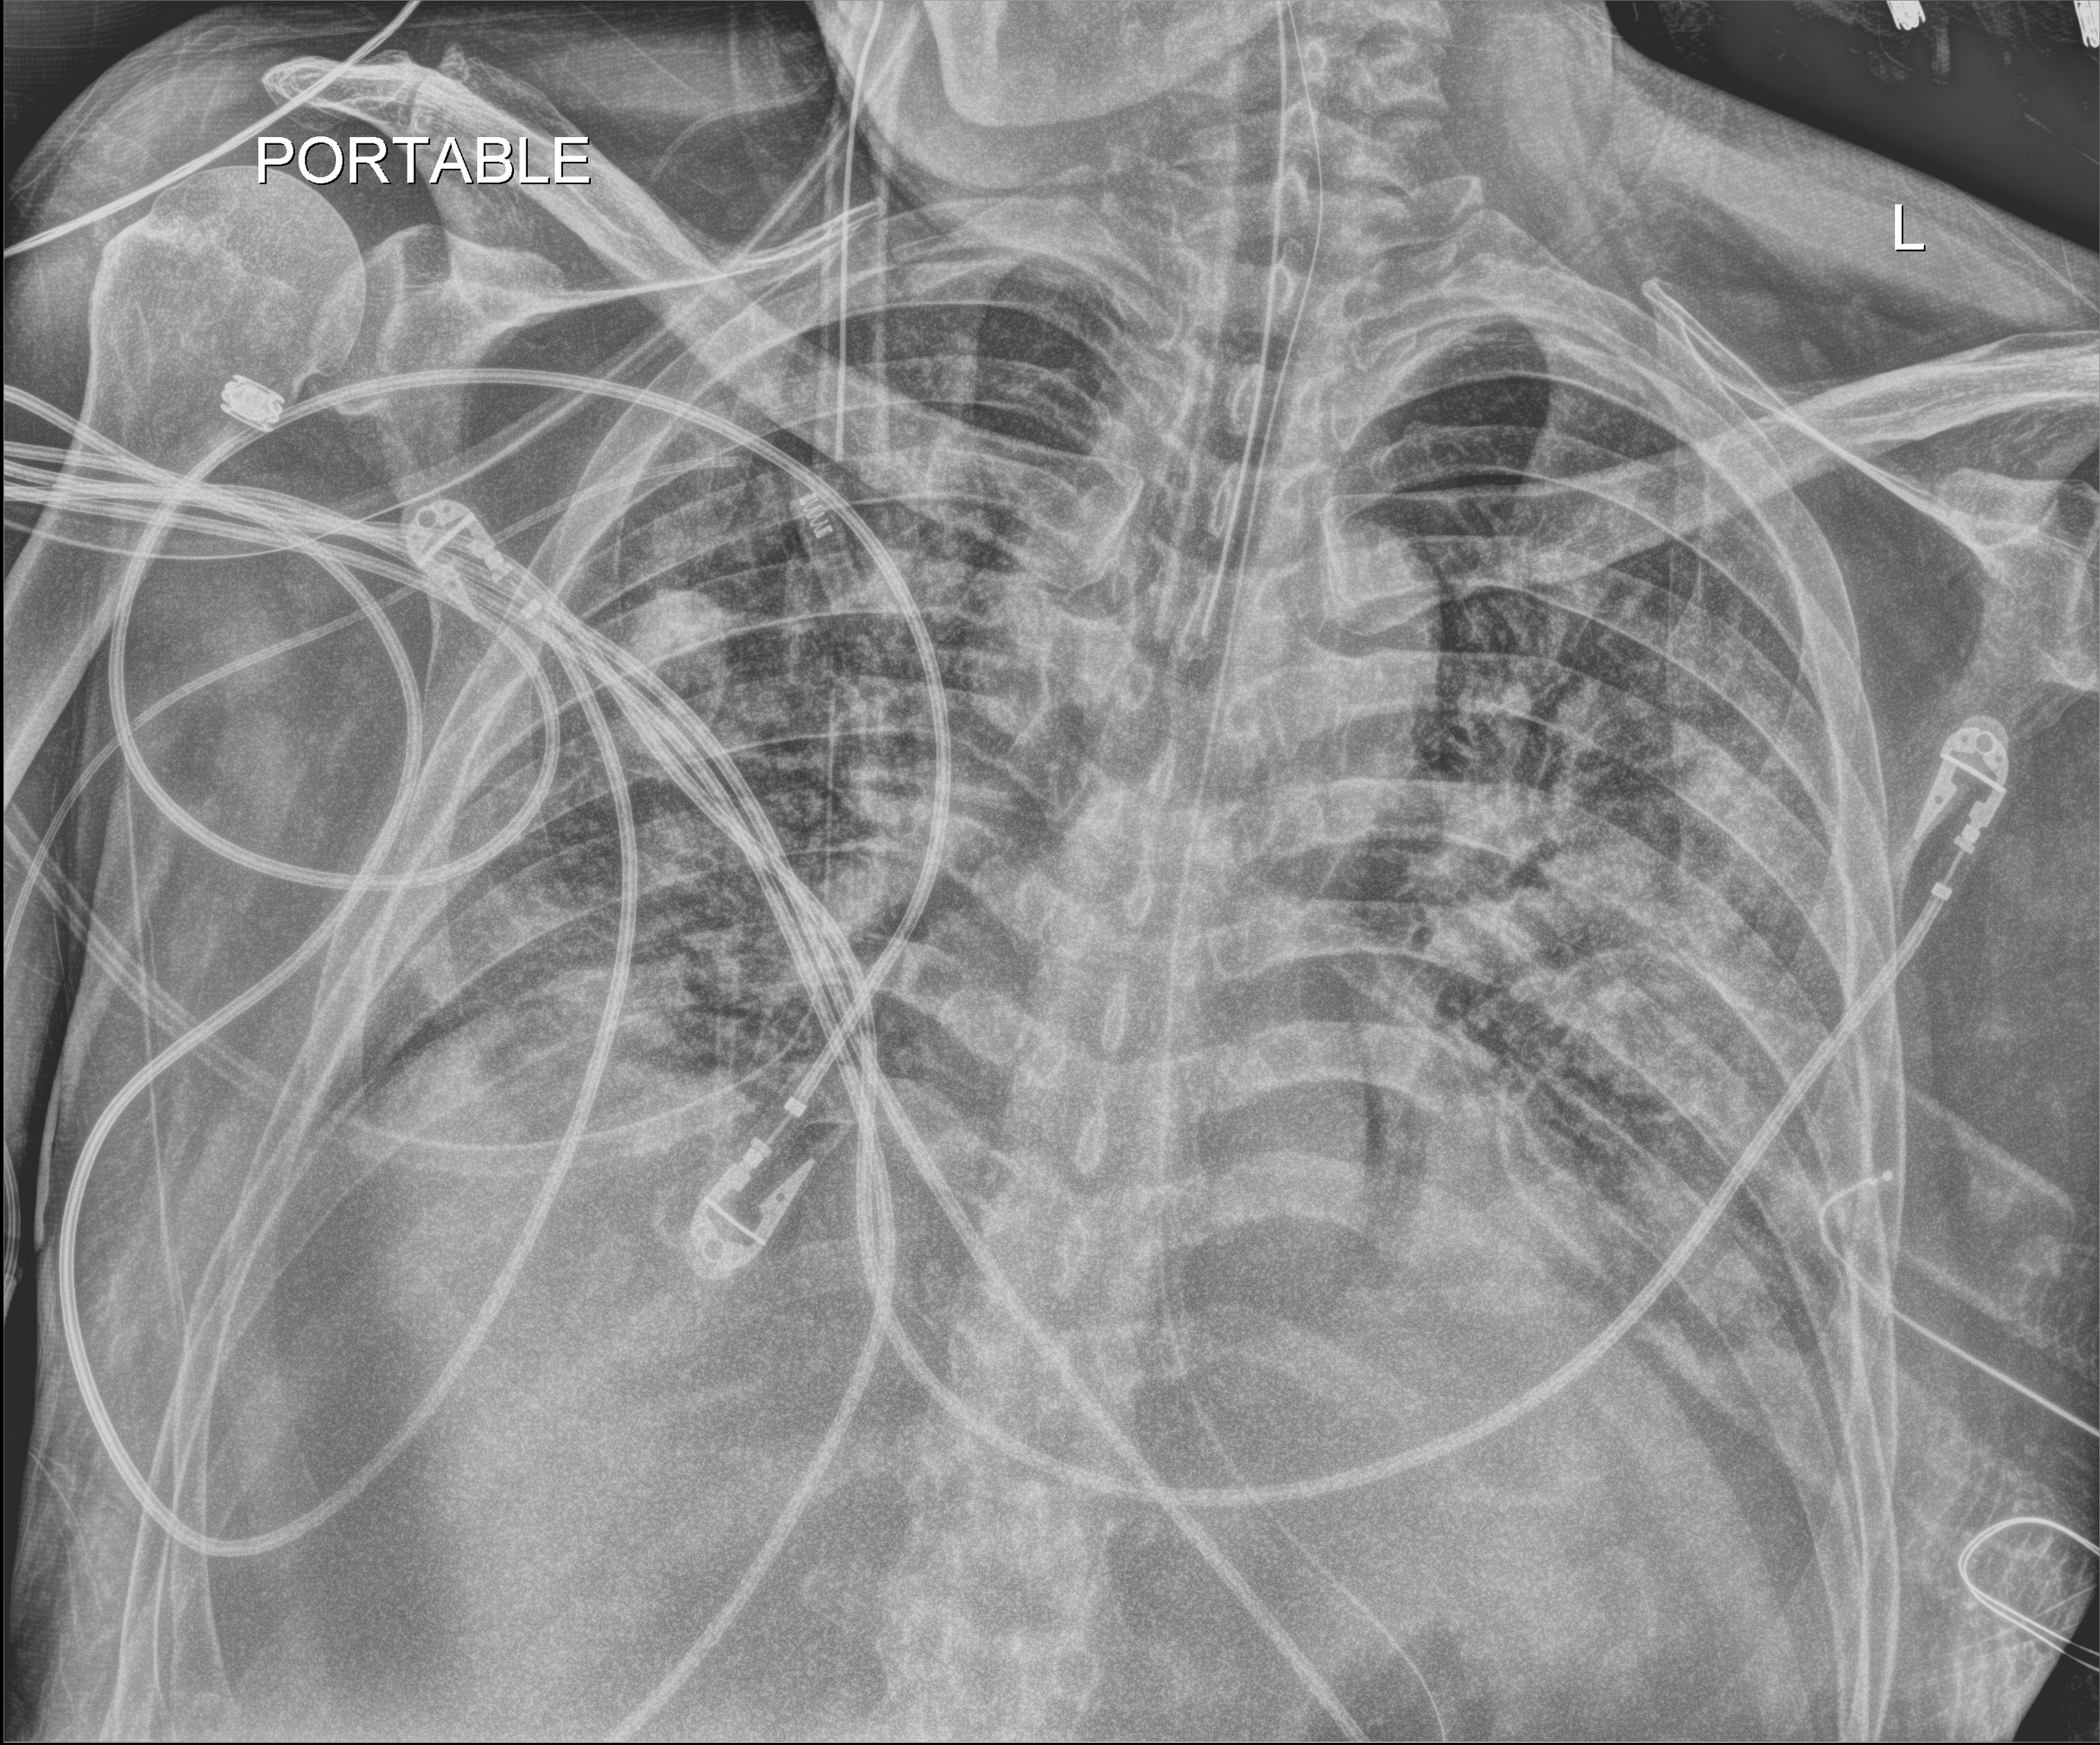
Portable chest radiograph. Male patient hospitalised with COVID-19, age 18–59 years.
Hospital-stay facts (about this admission, not read from this image; timing relative to this image not recorded): length of hospital stay: 40 days.